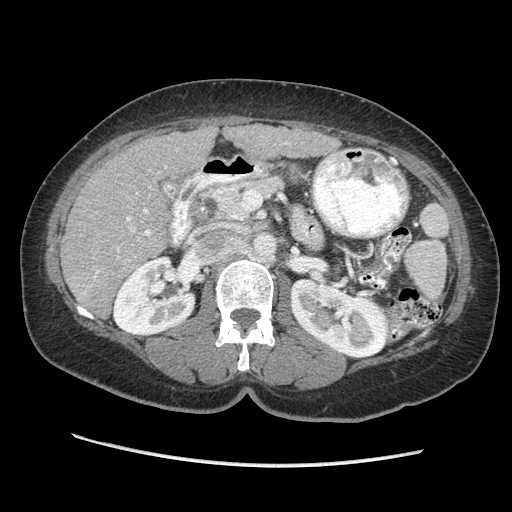
Contrast-enhanced abdominal CT (liver protocol), one axial slice. Position 116 of 170 along the scan axis. 140 kVp. Soft-tissue window (W 400 / L 40 HU). 512 × 512 image matrix. From the clinical record (not read from this slice): diagnosis: hepatocellular carcinoma (patient treated with transarterial chemoembolisation; whether this scan precedes or follows treatment is not stated here); TNM stage (as recorded): Stage-II; Child-Pugh class: A; tumour differentiation: no biopsy; tumour nodularity: multinodular.
Outlined on this slice (semi-automatic segmentation, software-assisted and operator-edited):
- liver parenchyma outside the tumour (the mass and vessels are separate outlines, so this box may not span the whole liver): bounding box <60,124,340,317> (left, top, right, bottom; pixels)
- liver vessels: <83,142,288,294>